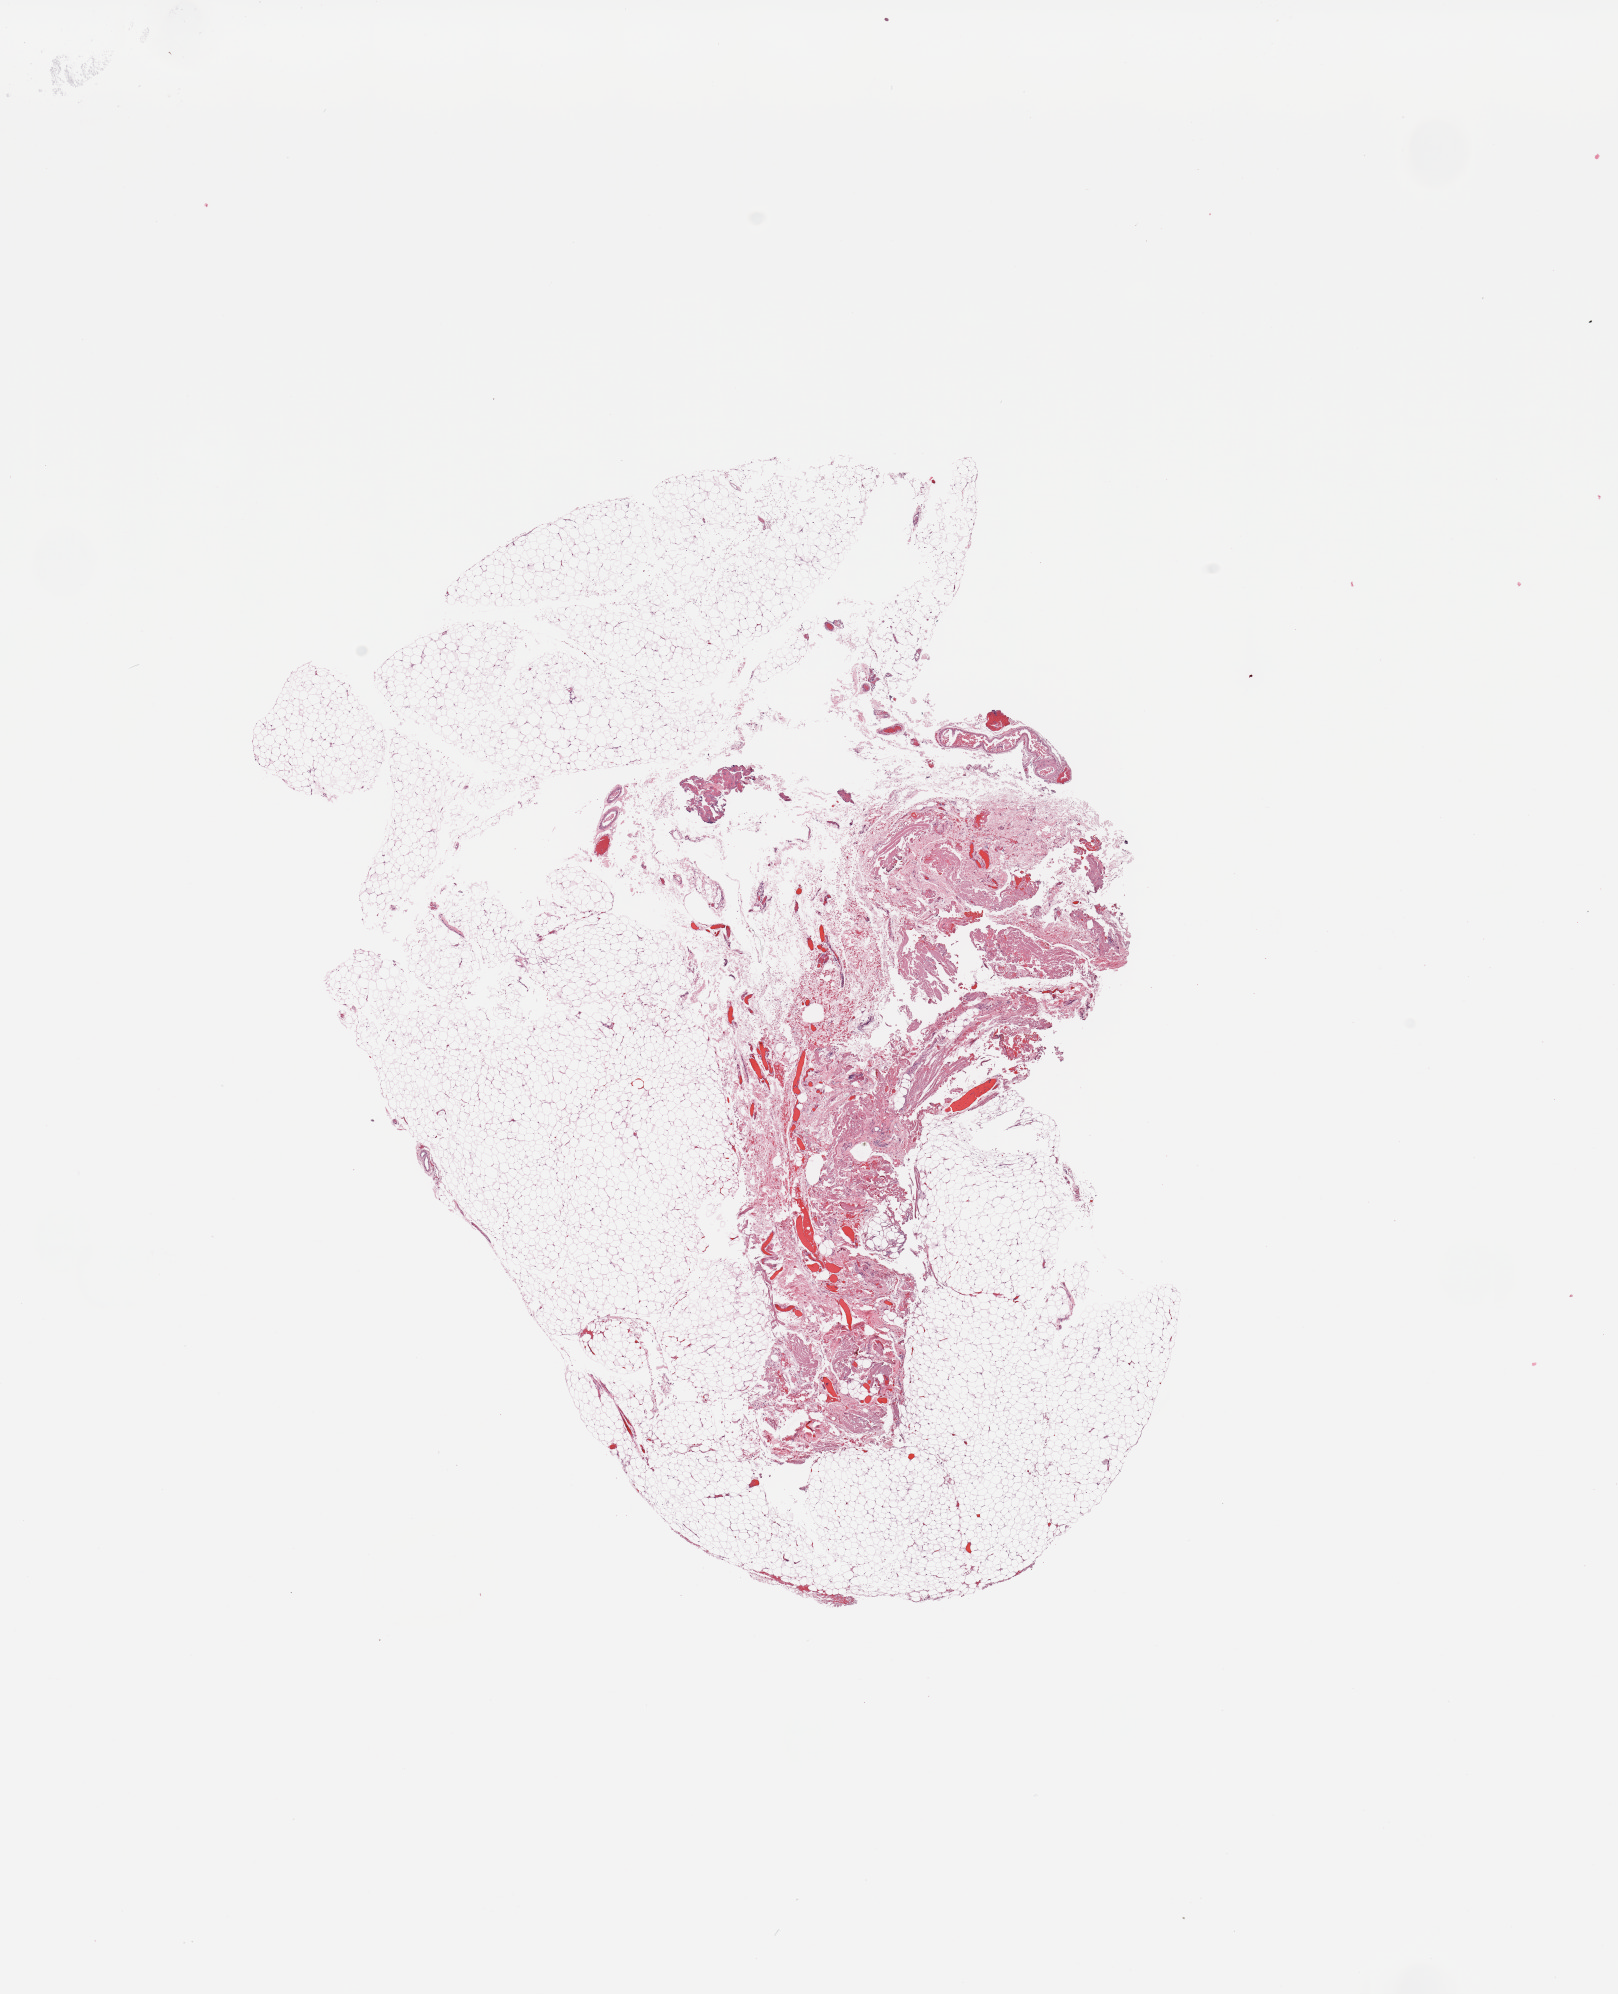
Hematoxylin and eosin (H&E) stained whole-slide image, low-resolution overview of the scanned area, about 12.8 x 15.8 mm; kidney, normal (non-tumour) tissue. 41-year-old male patient.
- this section: normal (non-tumour) tissue from the same patient
- patient diagnosis: Renal cell carcinoma, NOS